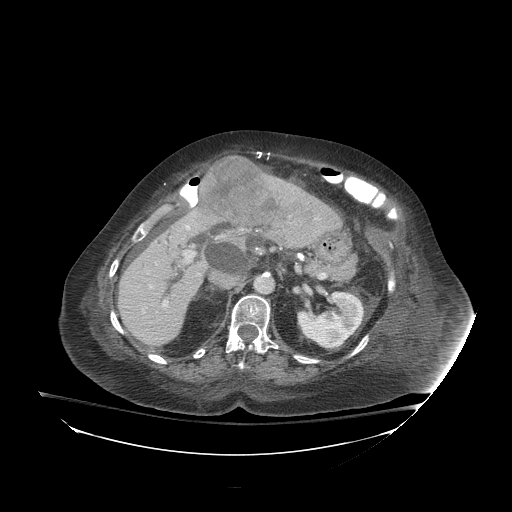
Contrast-enhanced abdominal CT (liver protocol), one axial slice; slice 47 of 81 in the series (ordered by position); reconstruction kernel STANDARD; 140 kVp; soft-tissue window (W 400 / L 40 HU); 2.5 mm slice thickness; 512 × 512 image matrix, field of view 500 × 500 mm. From the clinical record (not read from this slice): diagnosis: hepatocellular carcinoma (patient treated with transarterial chemoembolisation; whether this scan precedes or follows treatment is not stated here); TNM stage (as recorded): Stage-I; Child-Pugh class: B; tumour differentiation: well-moderately differentiated.
Annotated regions visible in this slice (semi-automatically segmented with operator editing):
- liver parenchyma outside the tumour (the mass and vessels are separate outlines, so this box may not span the whole liver): bounding box <118,175,341,346> (left, top, right, bottom; pixels)
- mass: <200,156,278,225>
- liver vessels: <150,225,195,307>